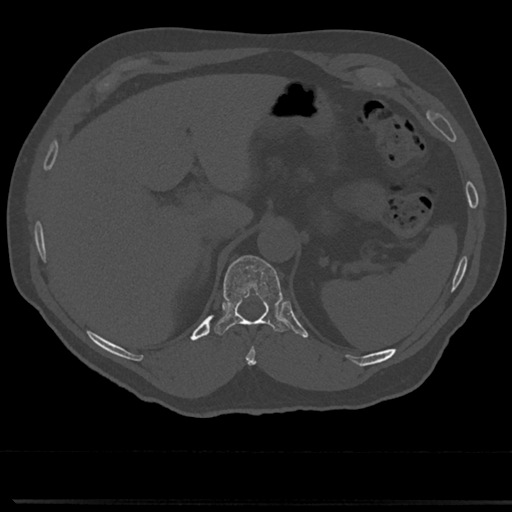
CT including the spine, one axial slice; slice 211 of 817 in the series (ordered by position); reconstruction kernel Br40s/3; 120 kVp; bone window (W 1800 / L 400 HU); 0.5 mm slice thickness; 512 × 512 image matrix, field of view 355 × 355 mm. Patient: male, 61 years. Case-level facts recorded for this patient, not image findings: primary cancer: prostate.
Annotated regions visible in this slice (semi-automatic segmentation, software-assisted and operator-edited):
- T10 vertebra: bounding box (x1, y1, x2, y2) in pixels: (246, 331, 259, 366)
- T11 vertebra: (214, 256, 289, 336)